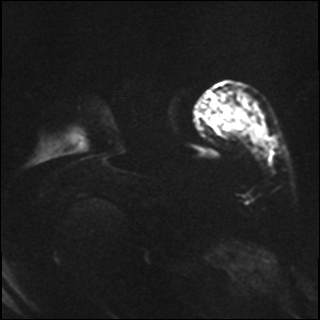
Breast MRI, one axial slice. Position 5 of 37 along the scan axis. Diffusion-weighted series; image 2 of 4 stored at this slice position (different b-values; order by instance number). 1.5 T. 4 mm slice thickness. 320 × 320 image matrix, field of view 320 × 320 mm. Female patient.
Annotated regions visible in this slice (outlined manually by an expert reader):
- tumour on diffusion-weighted imaging: bounding box (x1, y1, x2, y2) in pixels: (227, 107, 236, 122)